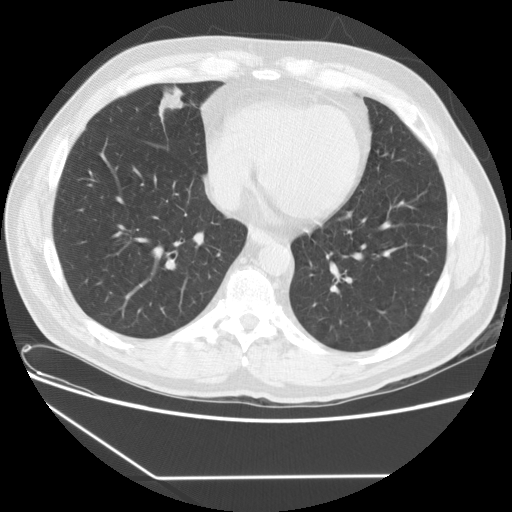
Axial slice from a low-dose chest CT screening exam, baseline screening round, lung window (W 1500 / L -600 HU), 2.5 mm slice thickness, standard (soft-tissue) reconstruction kernel (STANDARD), slice 104 of 154 in the series, 512 × 512 image matrix, field of view 370 × 370 mm. Male, age 59 years at enrolment. Current smoker at enrolment.
Expert reader's lesion annotation, bounding box <151,87,197,117> (left, top, right, bottom; pixels). No non-calcified nodule or mass ≥4 mm was recorded by the screening reader at this exam.